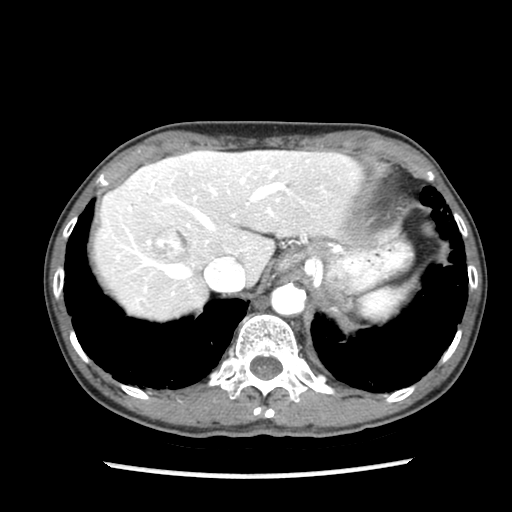
Contrast-enhanced abdominal CT (liver protocol), one axial slice; slice 66 of 87 in the series (ordered by position); reconstruction kernel STANDARD; soft-tissue window (W 400 / L 40 HU); 512 × 512 image matrix, field of view 300 × 300 mm. From the clinical record (not read from this slice): diagnosis: hepatocellular carcinoma (patient treated with transarterial chemoembolisation; whether this scan precedes or follows treatment is not stated here); TNM stage (as recorded): Stage-IIIB; Child-Pugh class: A; tumour differentiation: well differentiated; tumour nodularity: uninodular.
Annotated regions visible in this slice (semi-automatic segmentation, software-assisted and operator-edited):
- liver parenchyma outside the tumour (the mass and vessels are separate outlines, so this box may not span the whole liver): bounding box <94,150,362,320> (left, top, right, bottom; pixels)
- mass: <150,225,190,261>
- liver vessels: <117,156,284,279>